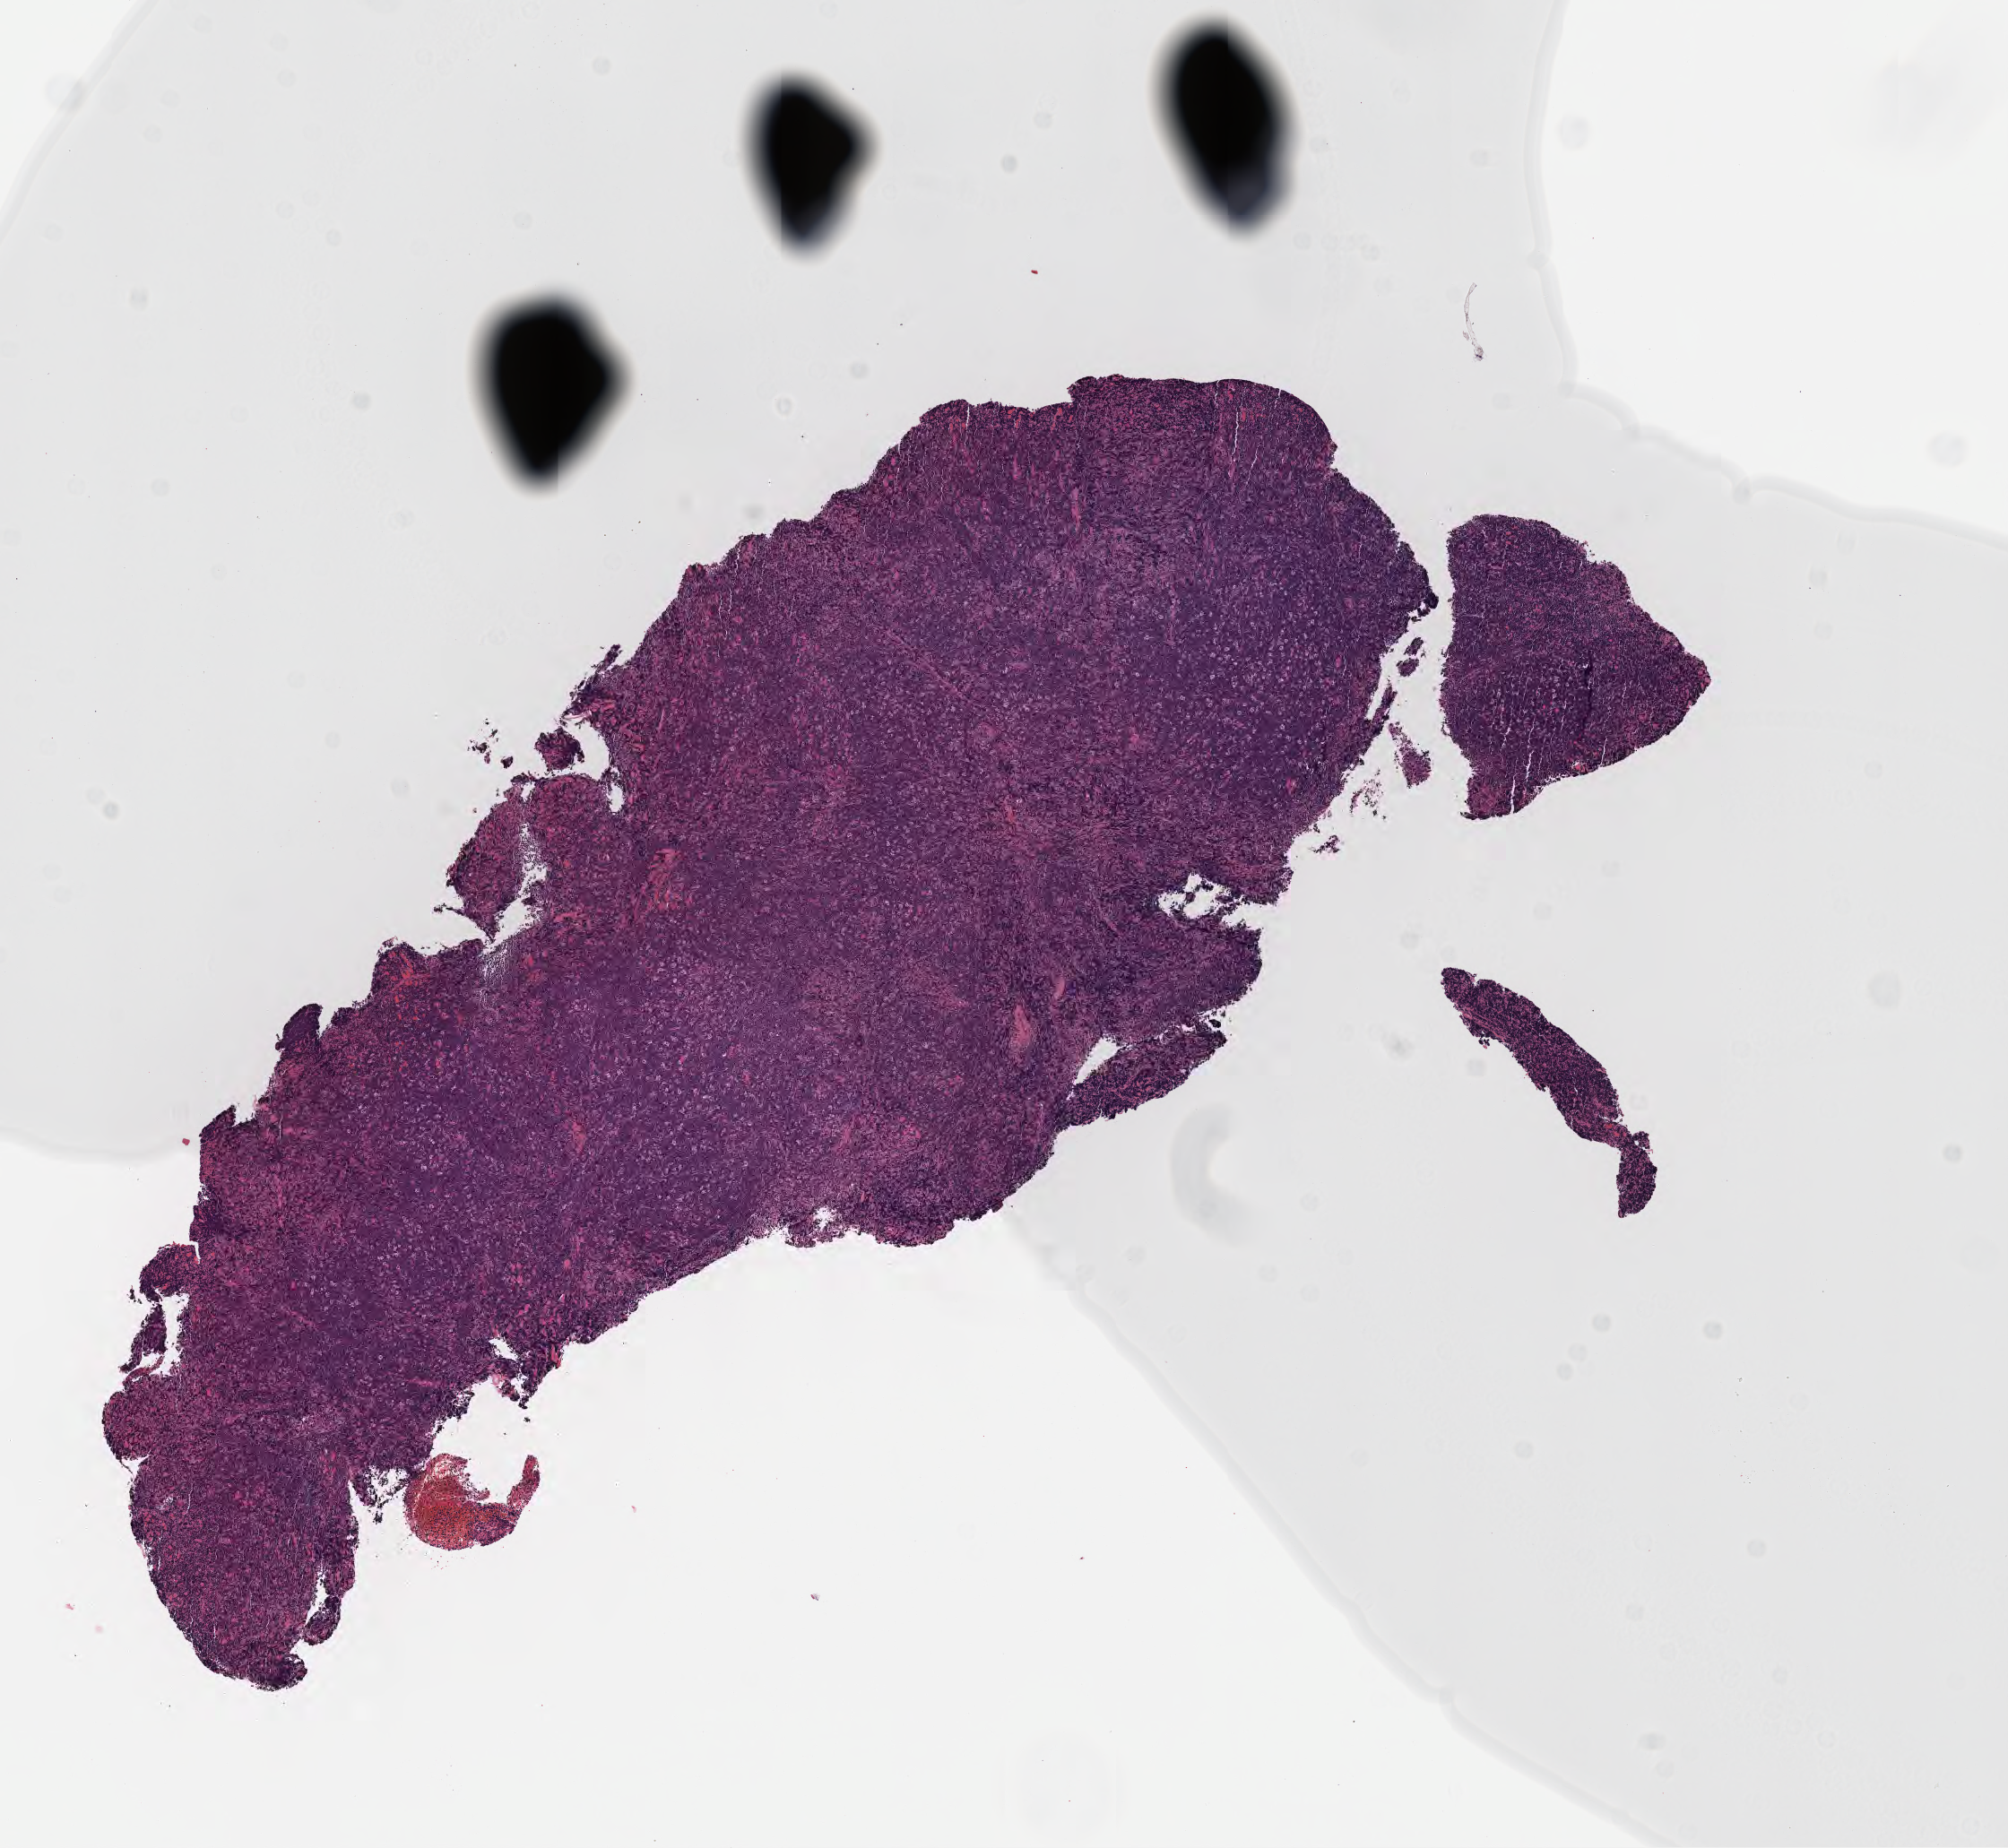
H&E whole-slide image — whole scanned area (about 9.1 x 8.3 mm) shown as a low-resolution overview; tumor tissue; site: lymph node of head and neck. Female patient, age 11 years.
Diagnosis: Burkitt lymphoma, NOS.